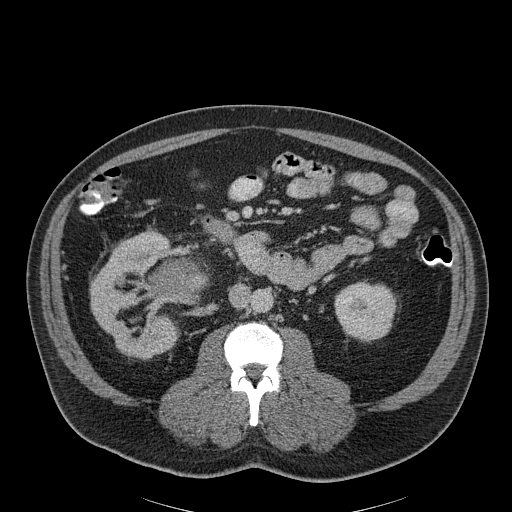
Contrast-enhanced abdominal CT, one axial slice; position 103 of 186 along the scan axis; 120 kVp; soft-tissue window (W 400 / L 40 HU); 3 mm slice thickness; 512 × 512 image matrix, field of view 464 × 464 mm. Patient: male, 56 years. From the clinical record (not read from this slice): diagnosis: adrenocortical carcinoma; tumour side: right adrenal; tumour size at pathology: 18 cm; Ki-67 index: 2 %; stage (as recorded): 3.
Structures marked on this image (semi-automatic segmentation, software-assisted and operator-edited):
- mass: box from (x=152, y=259) to (x=209, y=295) px